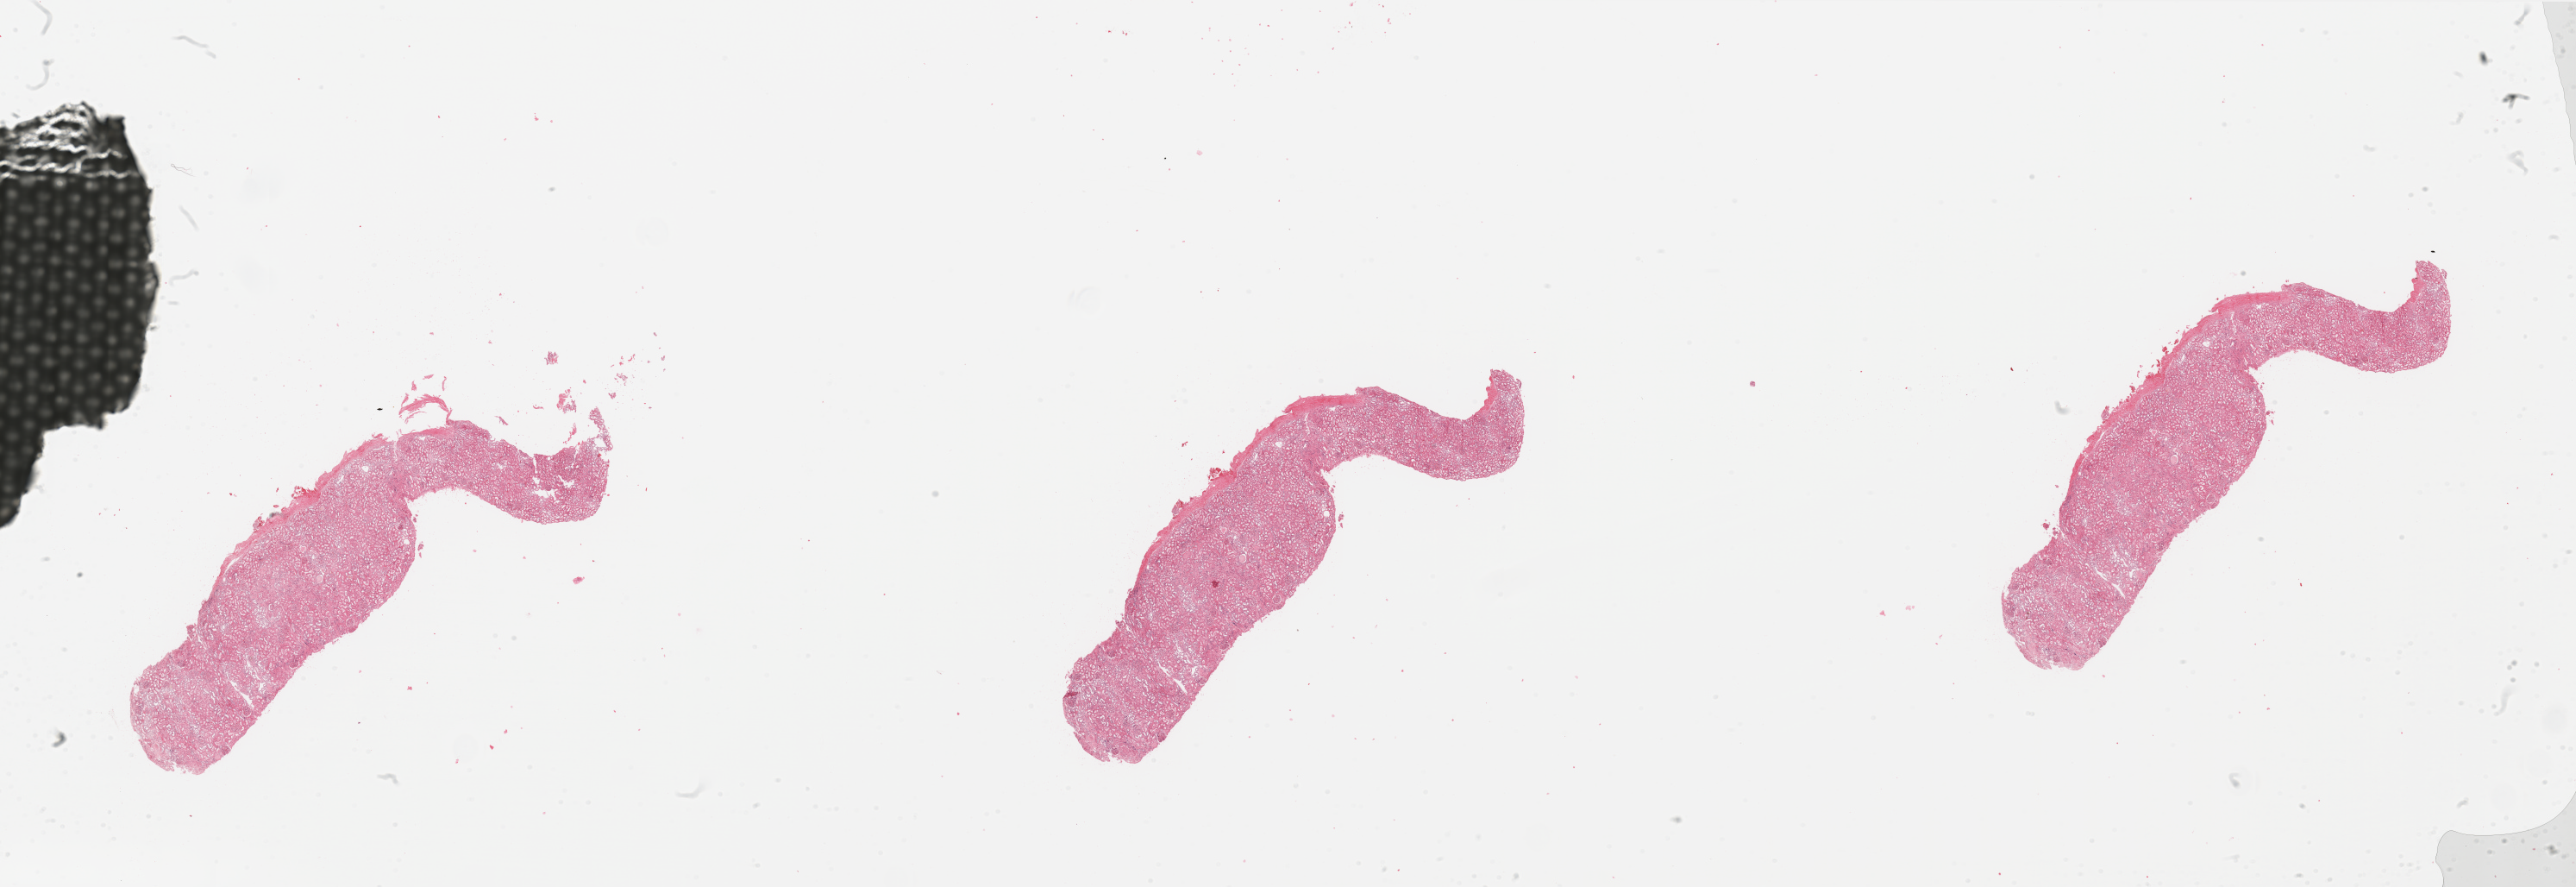
Digitized Hematoxylin and eosin (H&E) stained tissue section (whole slide), whole scanned area (about 47.3 x 16.3 mm, acquisition: 20x scan) shown as a low-resolution overview. Normal (non-tumour) tissue sample, kidney. Male, 56 y/o.
This section: normal (non-tumour) tissue from the same patient. Patient diagnosis: Renal cell carcinoma, NOS.